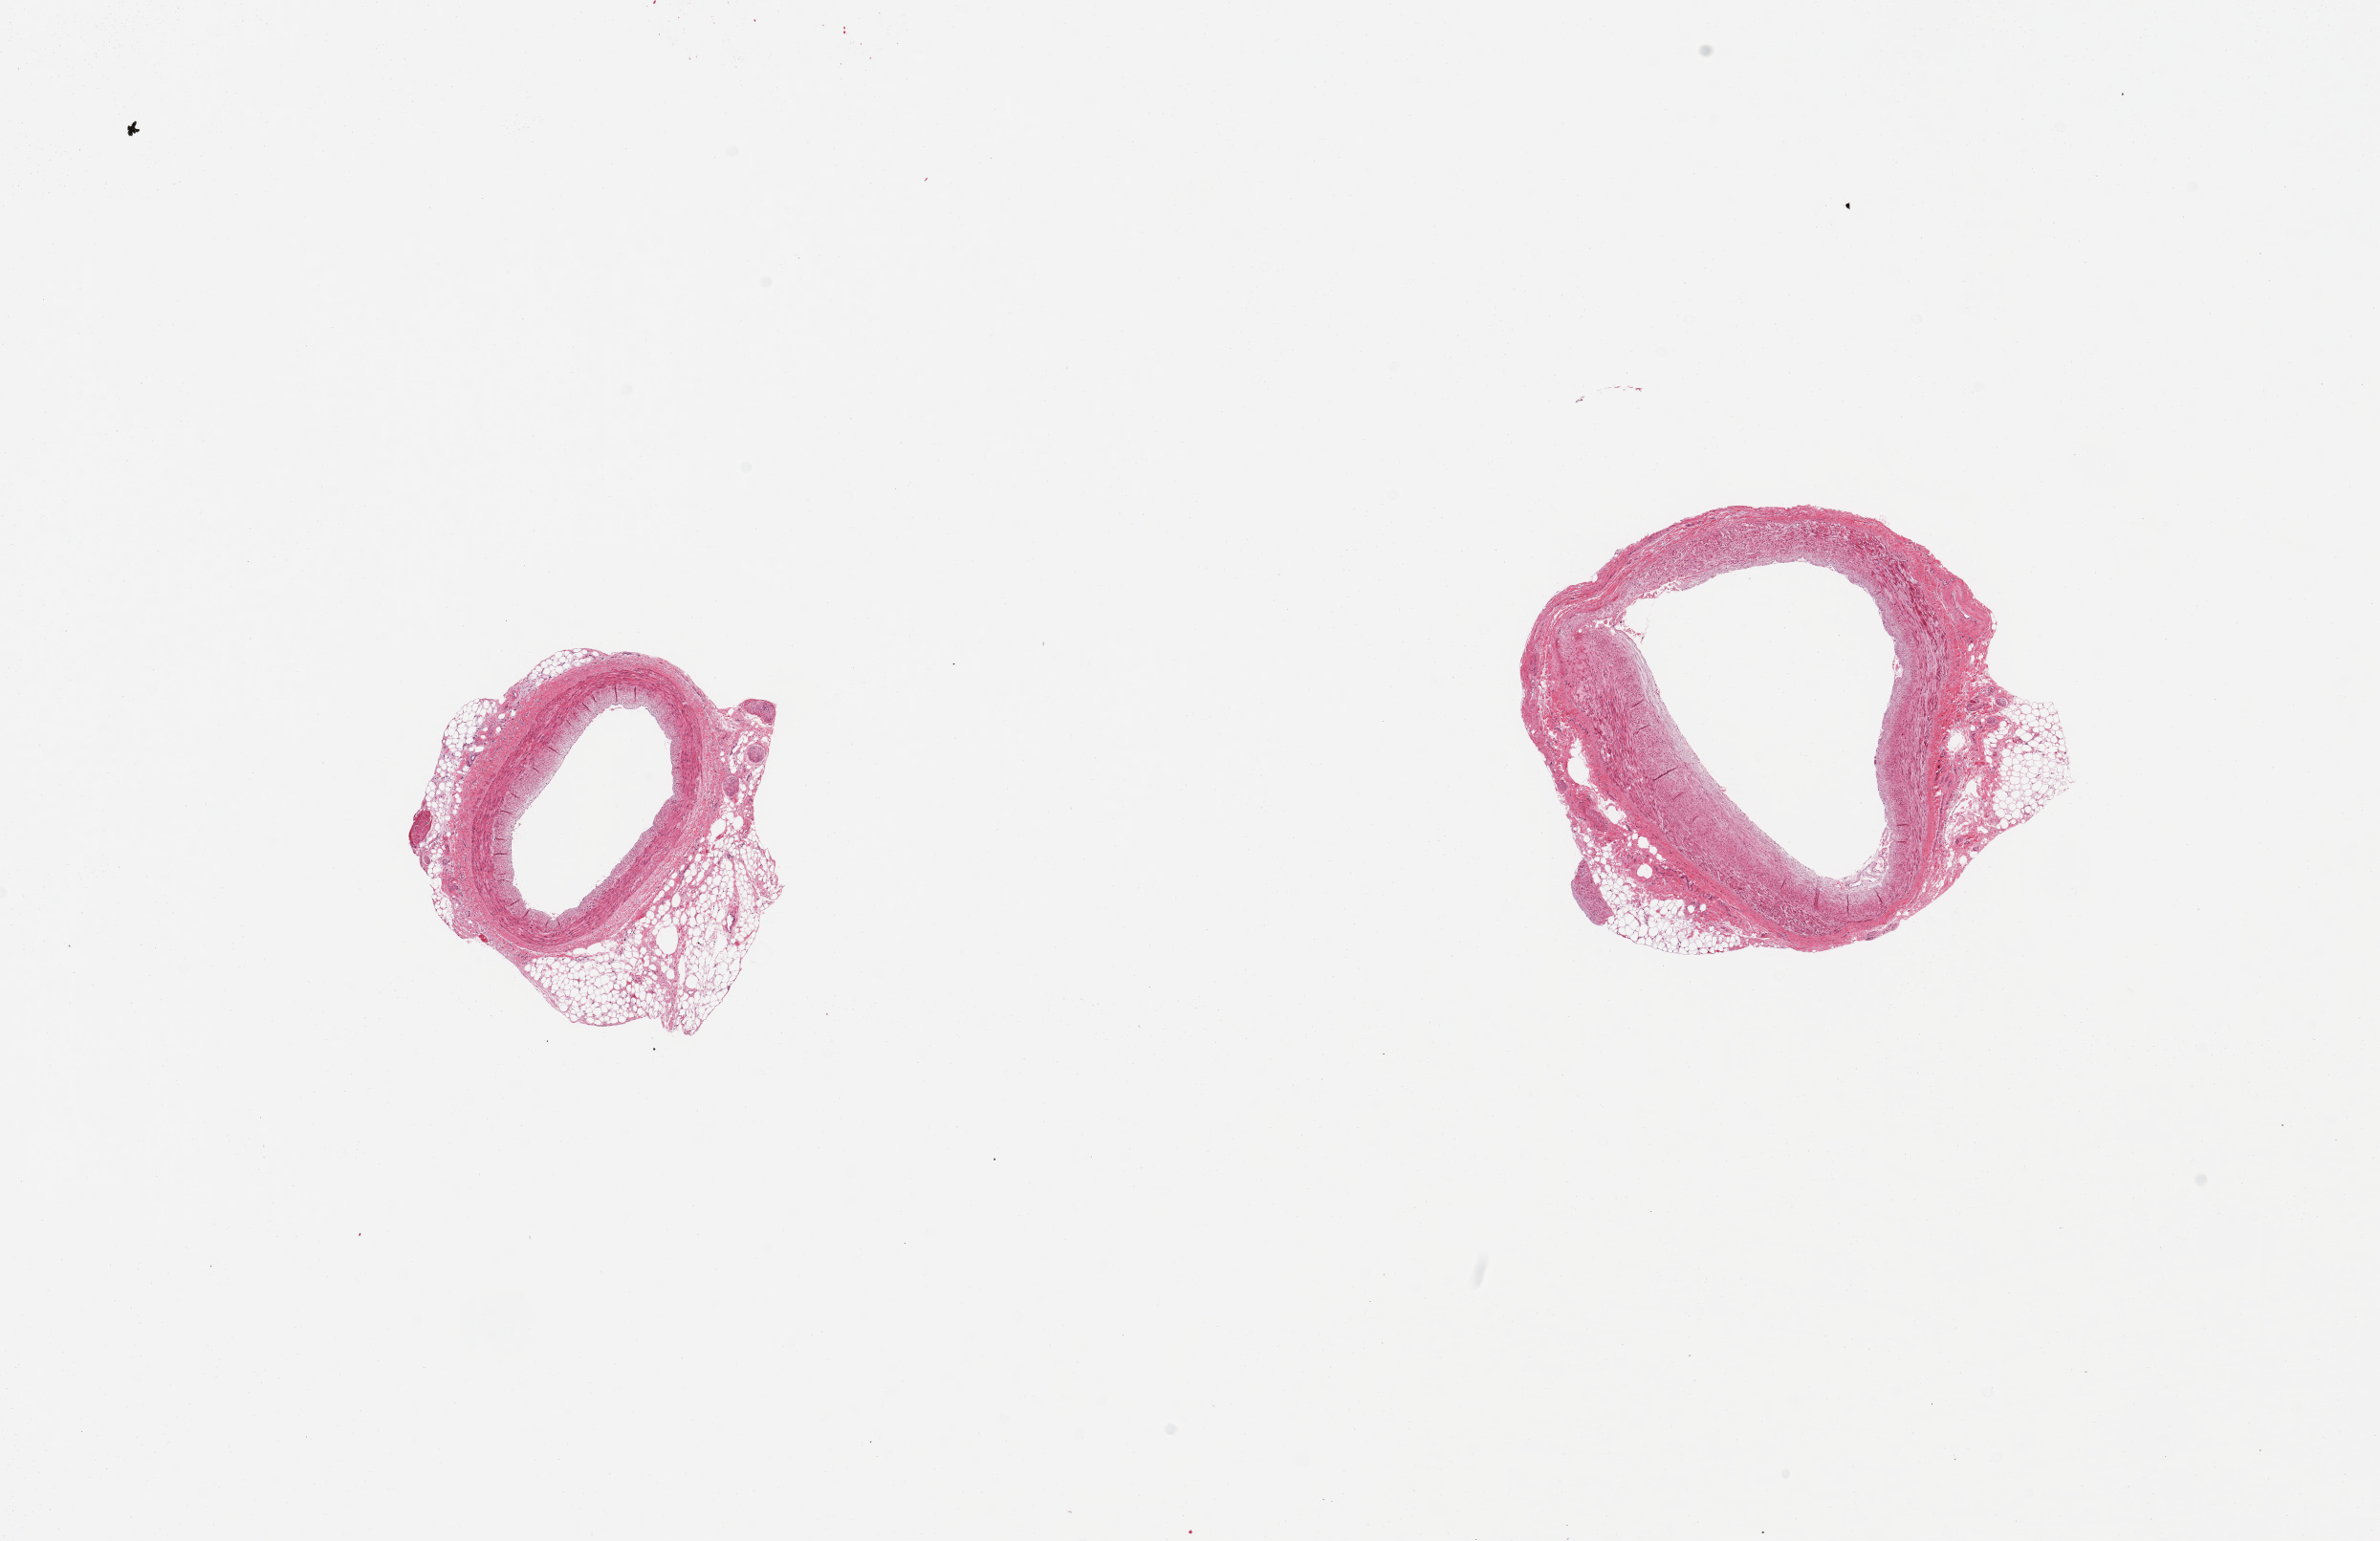
Hematoxylin and eosin (H&E) whole-slide image, a low-resolution overview of the entire scanned area, about 19.7 x 12.8 mm, PAXgene-fixed paraffin-embedded (PFPE) section, target tissue: coronary artery, tissue donor sample. Donor: female.
Reviewer comment on this tissue sample: 2 pieces; mild plaque.